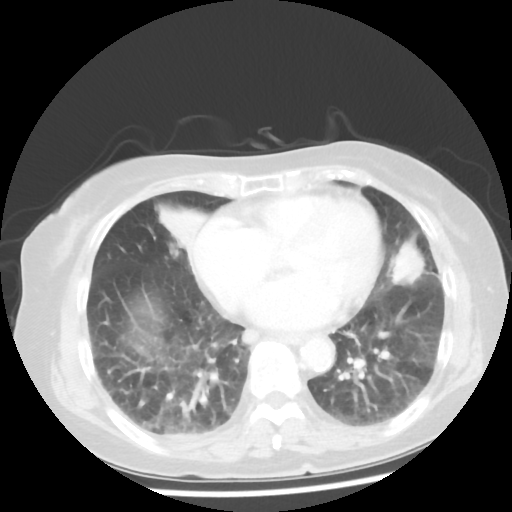
Chest CT, one axial slice; slice 17 of 50 in the series (ordered by position); reconstruction kernel STANDARD; 100 kVp; lung window (W 1500 / L -600 HU); 5 mm slice thickness; 512 × 512 image matrix, field of view 332 × 332 mm. Patient: female, 77 years. Case-level facts recorded for this patient, not image findings: clinical TNM (as recorded): T2 N3 M1a.
Annotated regions visible in this slice (rectangle marked by the reading radiologist):
- lung tumour (recorded histology: adenocarcinoma): bounding box <387,235,433,295> (left, top, right, bottom; pixels)